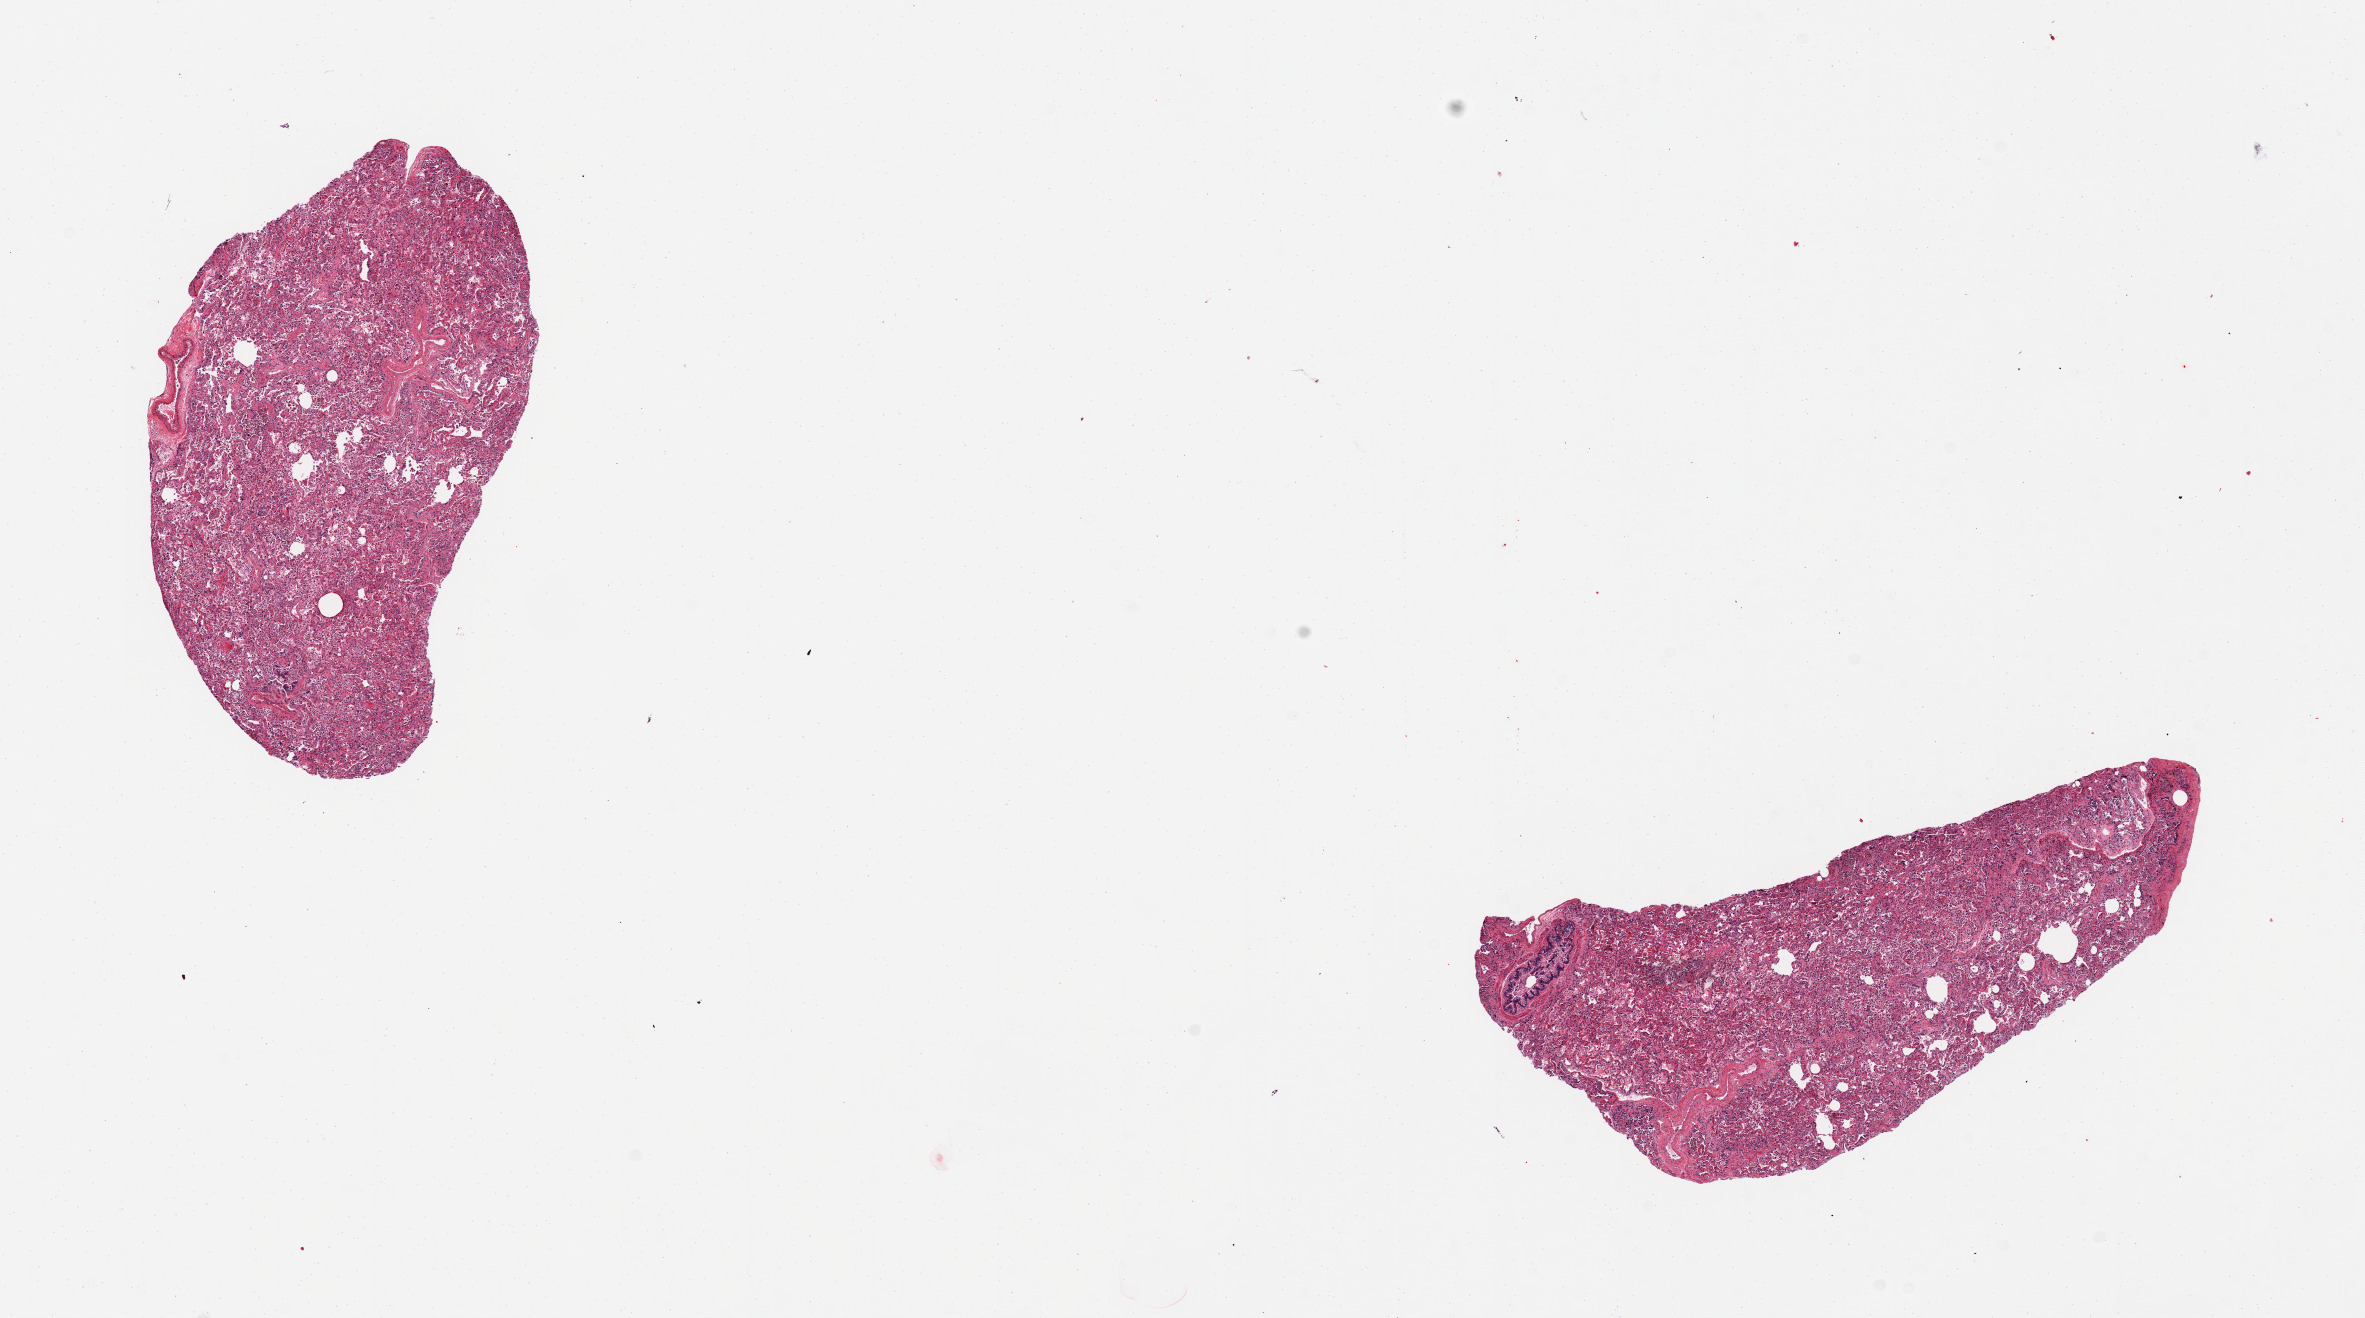
Digitized haematoxylin and eosin-stained section — low-resolution overview of the scanned area, about 18.7 x 10.4 mm, PAXgene-fixed, paraffin-embedded tissue, sampled site (target tissue): lung, tissue donor sample. Donor sex: female.
Pathologist's review note for this sample: 2 pieces, hemosiderin-laden macrophages, some interstitial fibrosis and hypertrophy of mucin-secreting cells.